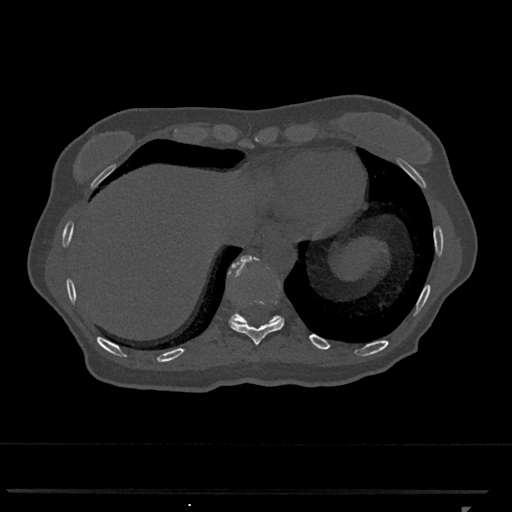
CT including the spine, one axial slice; slice 557 of 793 in the series (ordered by position); reconstruction kernel Br40s/3; 120 kVp; bone window (W 1800 / L 400 HU); 0.5 mm slice thickness; 512 × 512 image matrix, field of view 380 × 380 mm. Patient: female, 62 years. Case-level facts recorded for this patient, not image findings: primary cancer: renal.
Structures marked on this image (semi-automatic segmentation, software-assisted and operator-edited):
- T10 vertebra: bounding box [x1, y1, x2, y2] px = [229, 268, 284, 345]
- T11 vertebra: [228, 255, 282, 324]